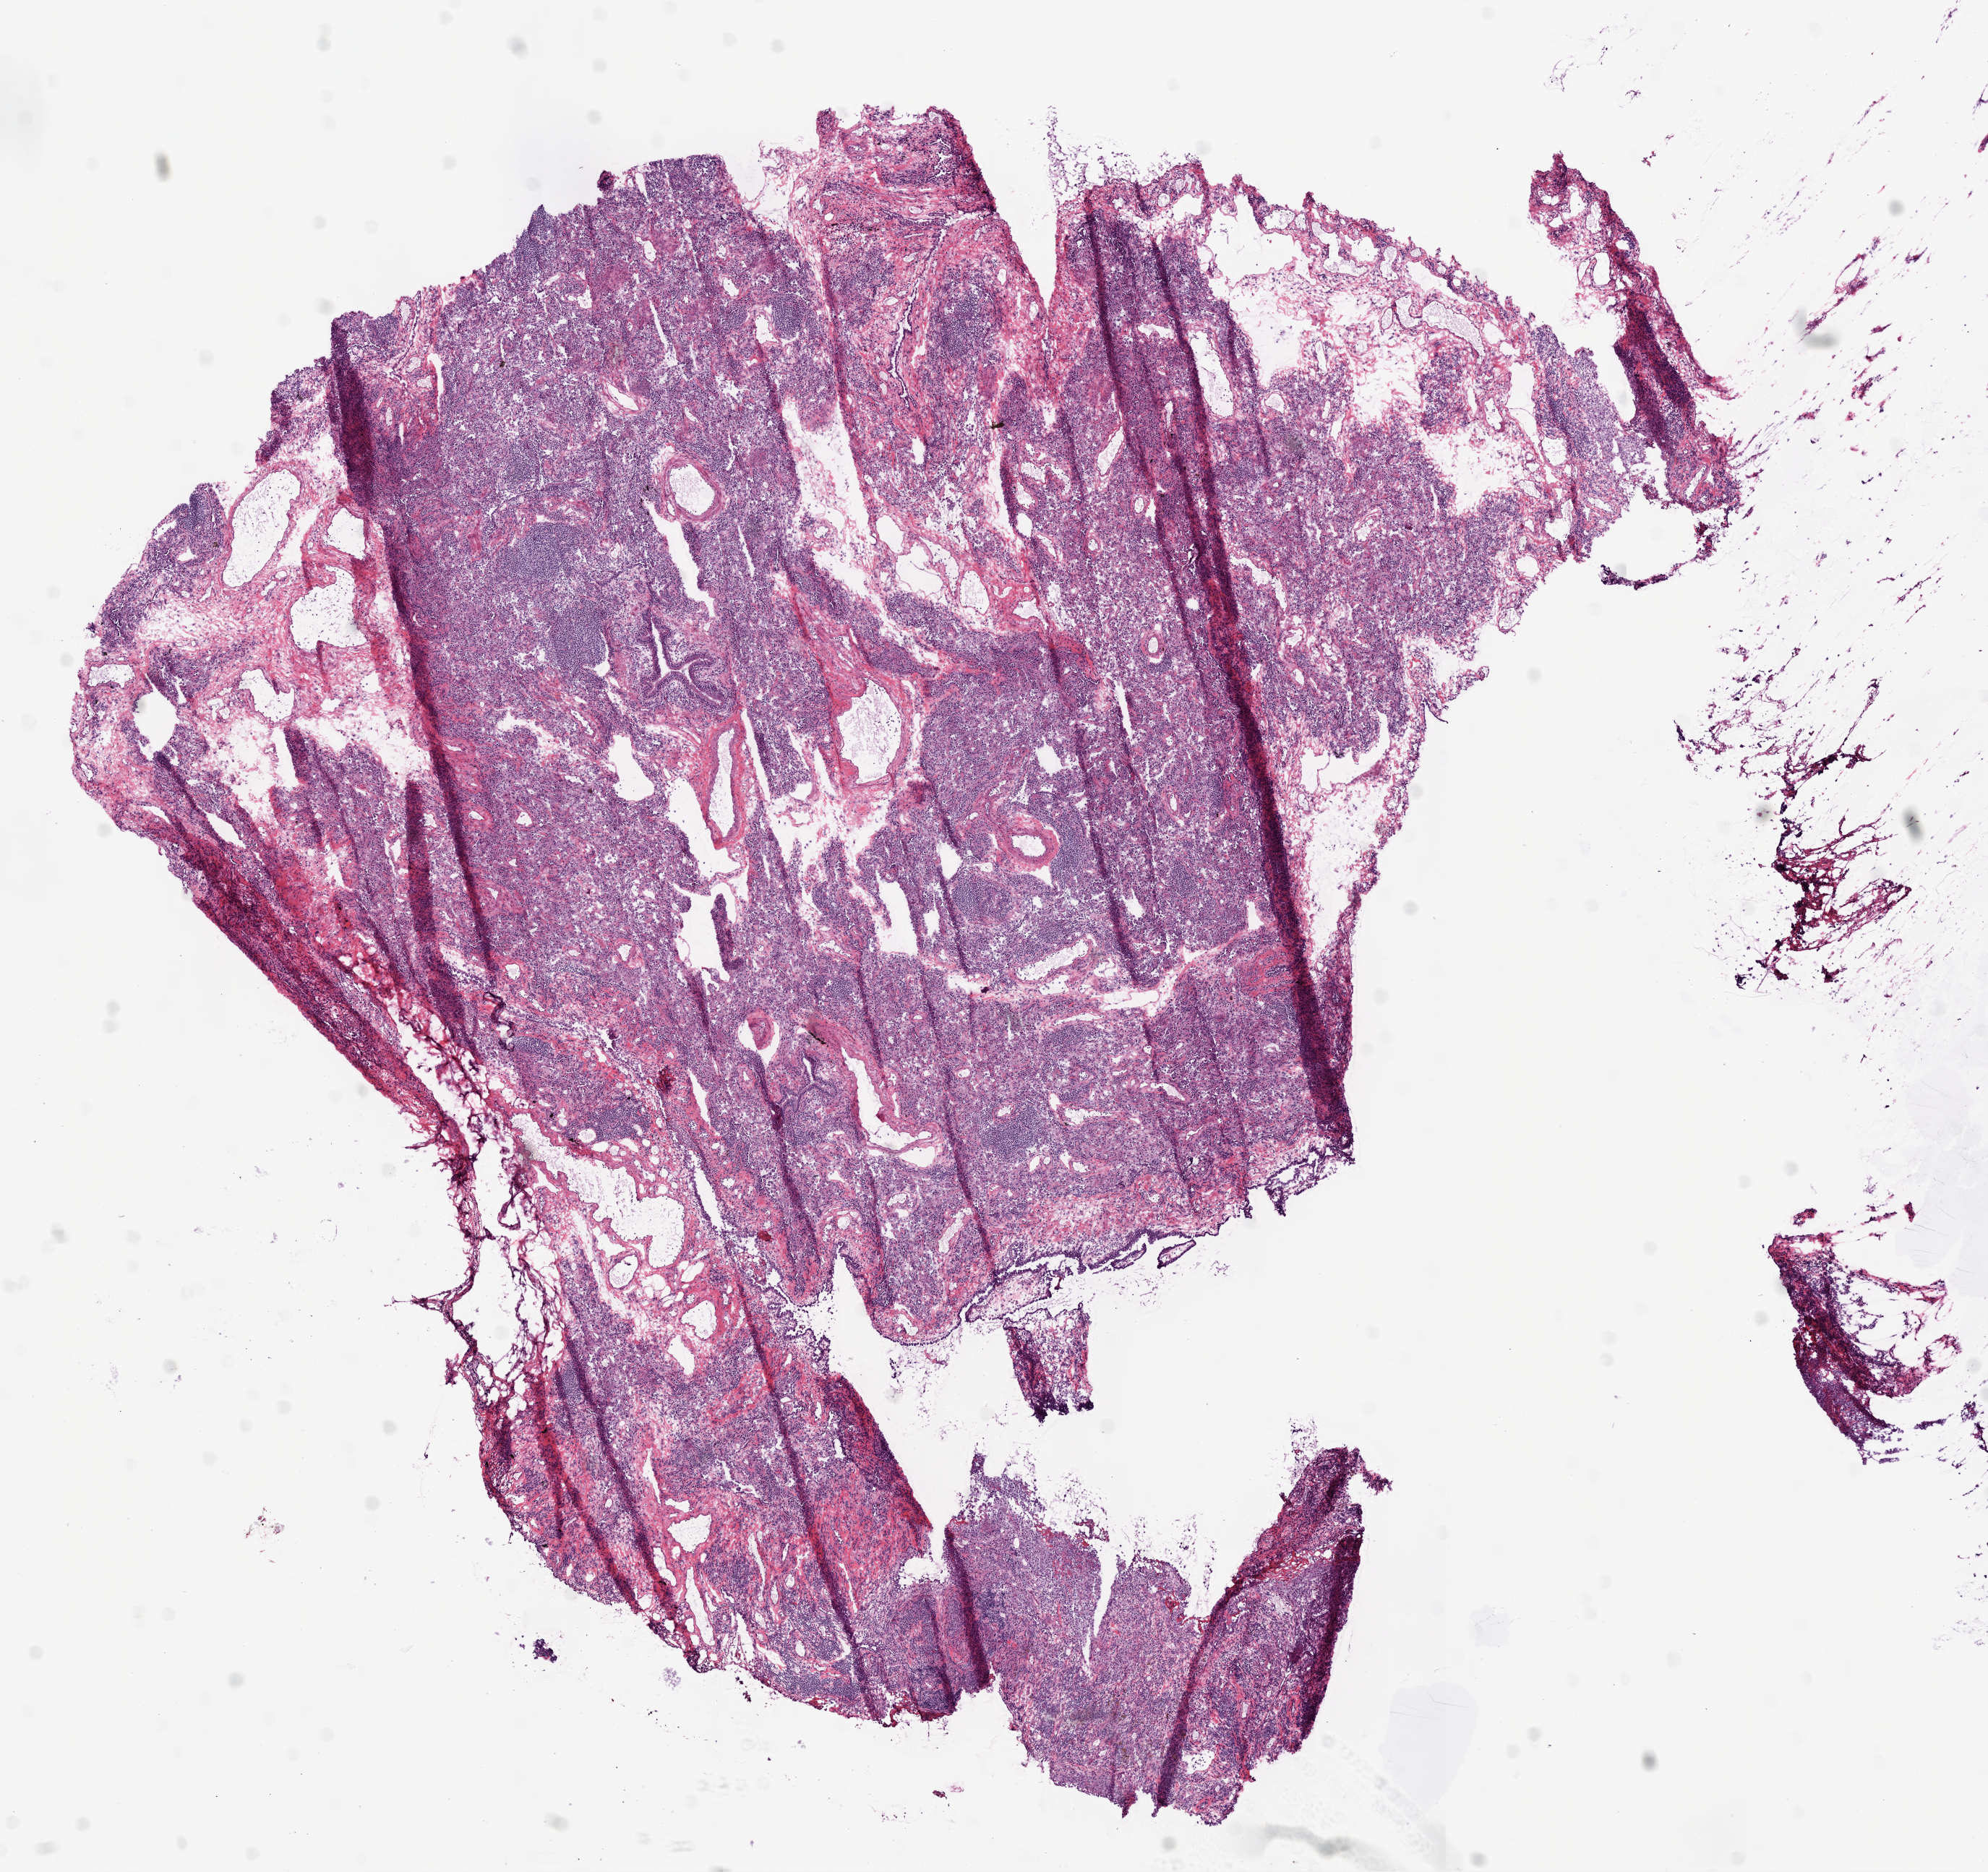
Whole-slide histology image, H&E, shown as a low-resolution overview of the whole scanned area (about 11.0 x 10.4 mm). Frozen section from the bottom of the tissue portion. Lung, solid tissue normal (non-tumour tissue) sample. Male, age 75 years at initial diagnosis.
This section: solid tissue normal sample (biorepository sample class). Patient diagnosis: Squamous cell carcinoma, NOS (upper lobe, lung).